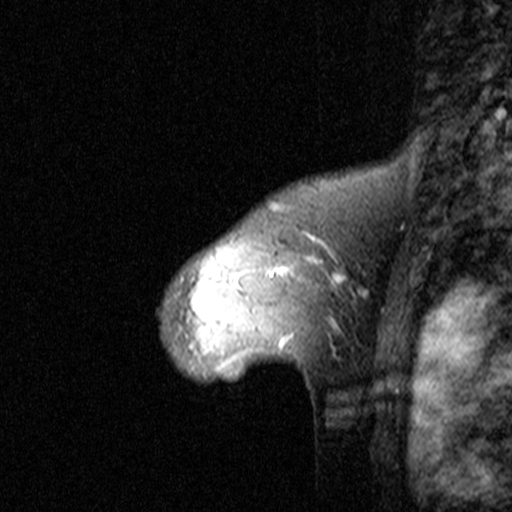
Breast MRI (dynamic contrast-enhanced), one sagittal slice; position 33 of 44 along the scan axis; dynamic contrast-enhanced study with each time point stored as its own series, time point 2 of 3 at this slice position (early post-contrast, ordered by acquisition time); 1.5 T; TE 4.5 ms, TR 11 ms; 512 × 512 image matrix. Female patient, age 46 years. From the clinical record (not read from this slice): setting: breast cancer imaged before/during neoadjuvant chemotherapy; receptor status: HER2-positive.
Structures marked on this image (semi-automatic segmentation, software-assisted and operator-edited):
- analysis volume of interest (the breast-tissue region the enhancement analysis was run in; not a lesion): bounding box [x1, y1, x2, y2] px = [149, 172, 359, 393]
- tumour enhancement mask (voxels above the 90 % enhancement threshold inside the analysis volume of interest): [234, 241, 346, 346]